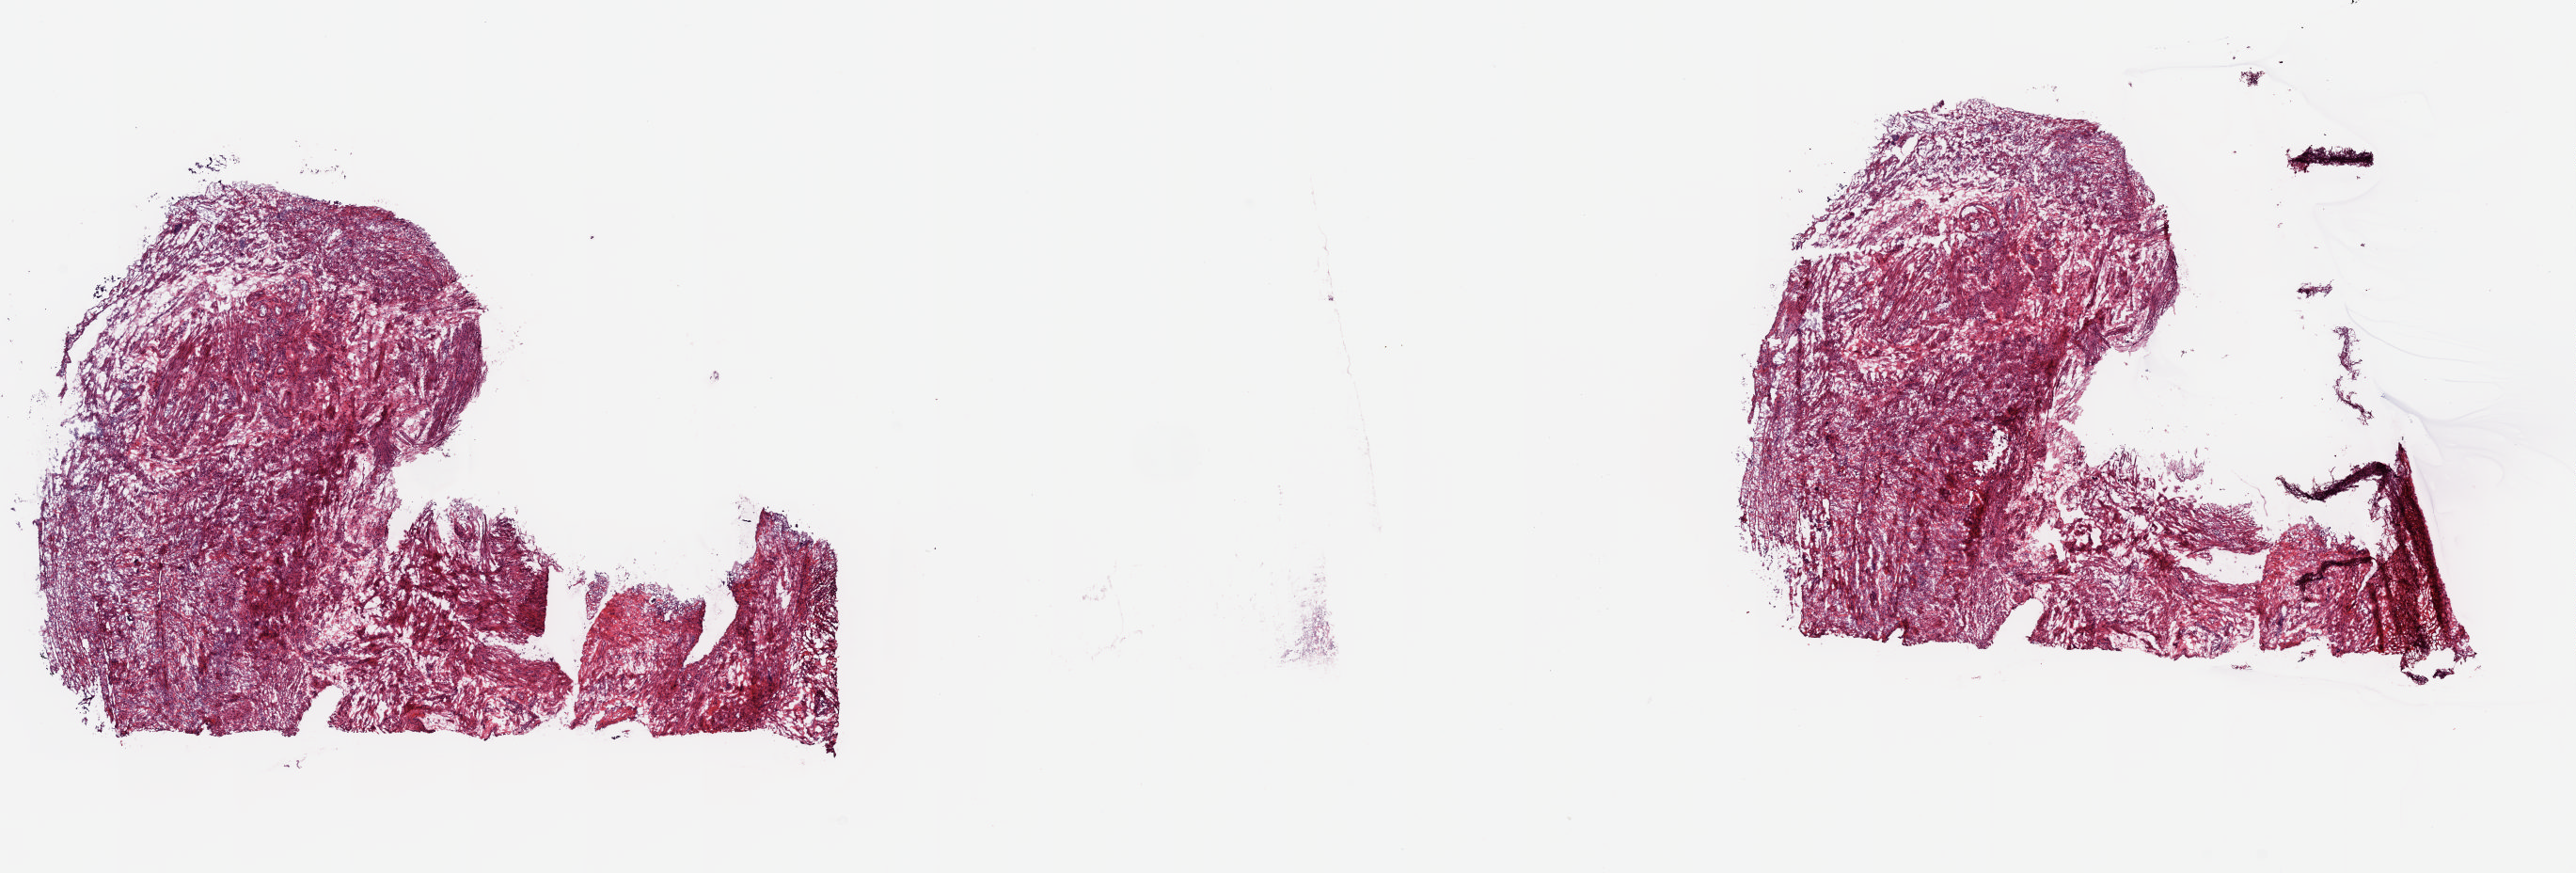
Whole-slide histology image, H&E-stained, whole scanned area (about 21.6 x 7.3 mm) shown as a low-resolution overview, frozen section, sample: solid tissue normal (non-tumour tissue), uterus. Female, age 35 years at initial diagnosis. Pathologist review of this section (percent, as recorded): tumour cells 0%, tumour nuclei 0%, normal cells 99%, stromal cells 0%, necrosis 1%. Inflammatory infiltration, as recorded: lymphocyte infiltration 1%, monocyte infiltration 0%, neutrophil infiltration 0%.
This section: solid tissue normal (non-tumour) sample from the same patient. Patient diagnosis: Endometrioid adenocarcinoma, NOS (endometrium).